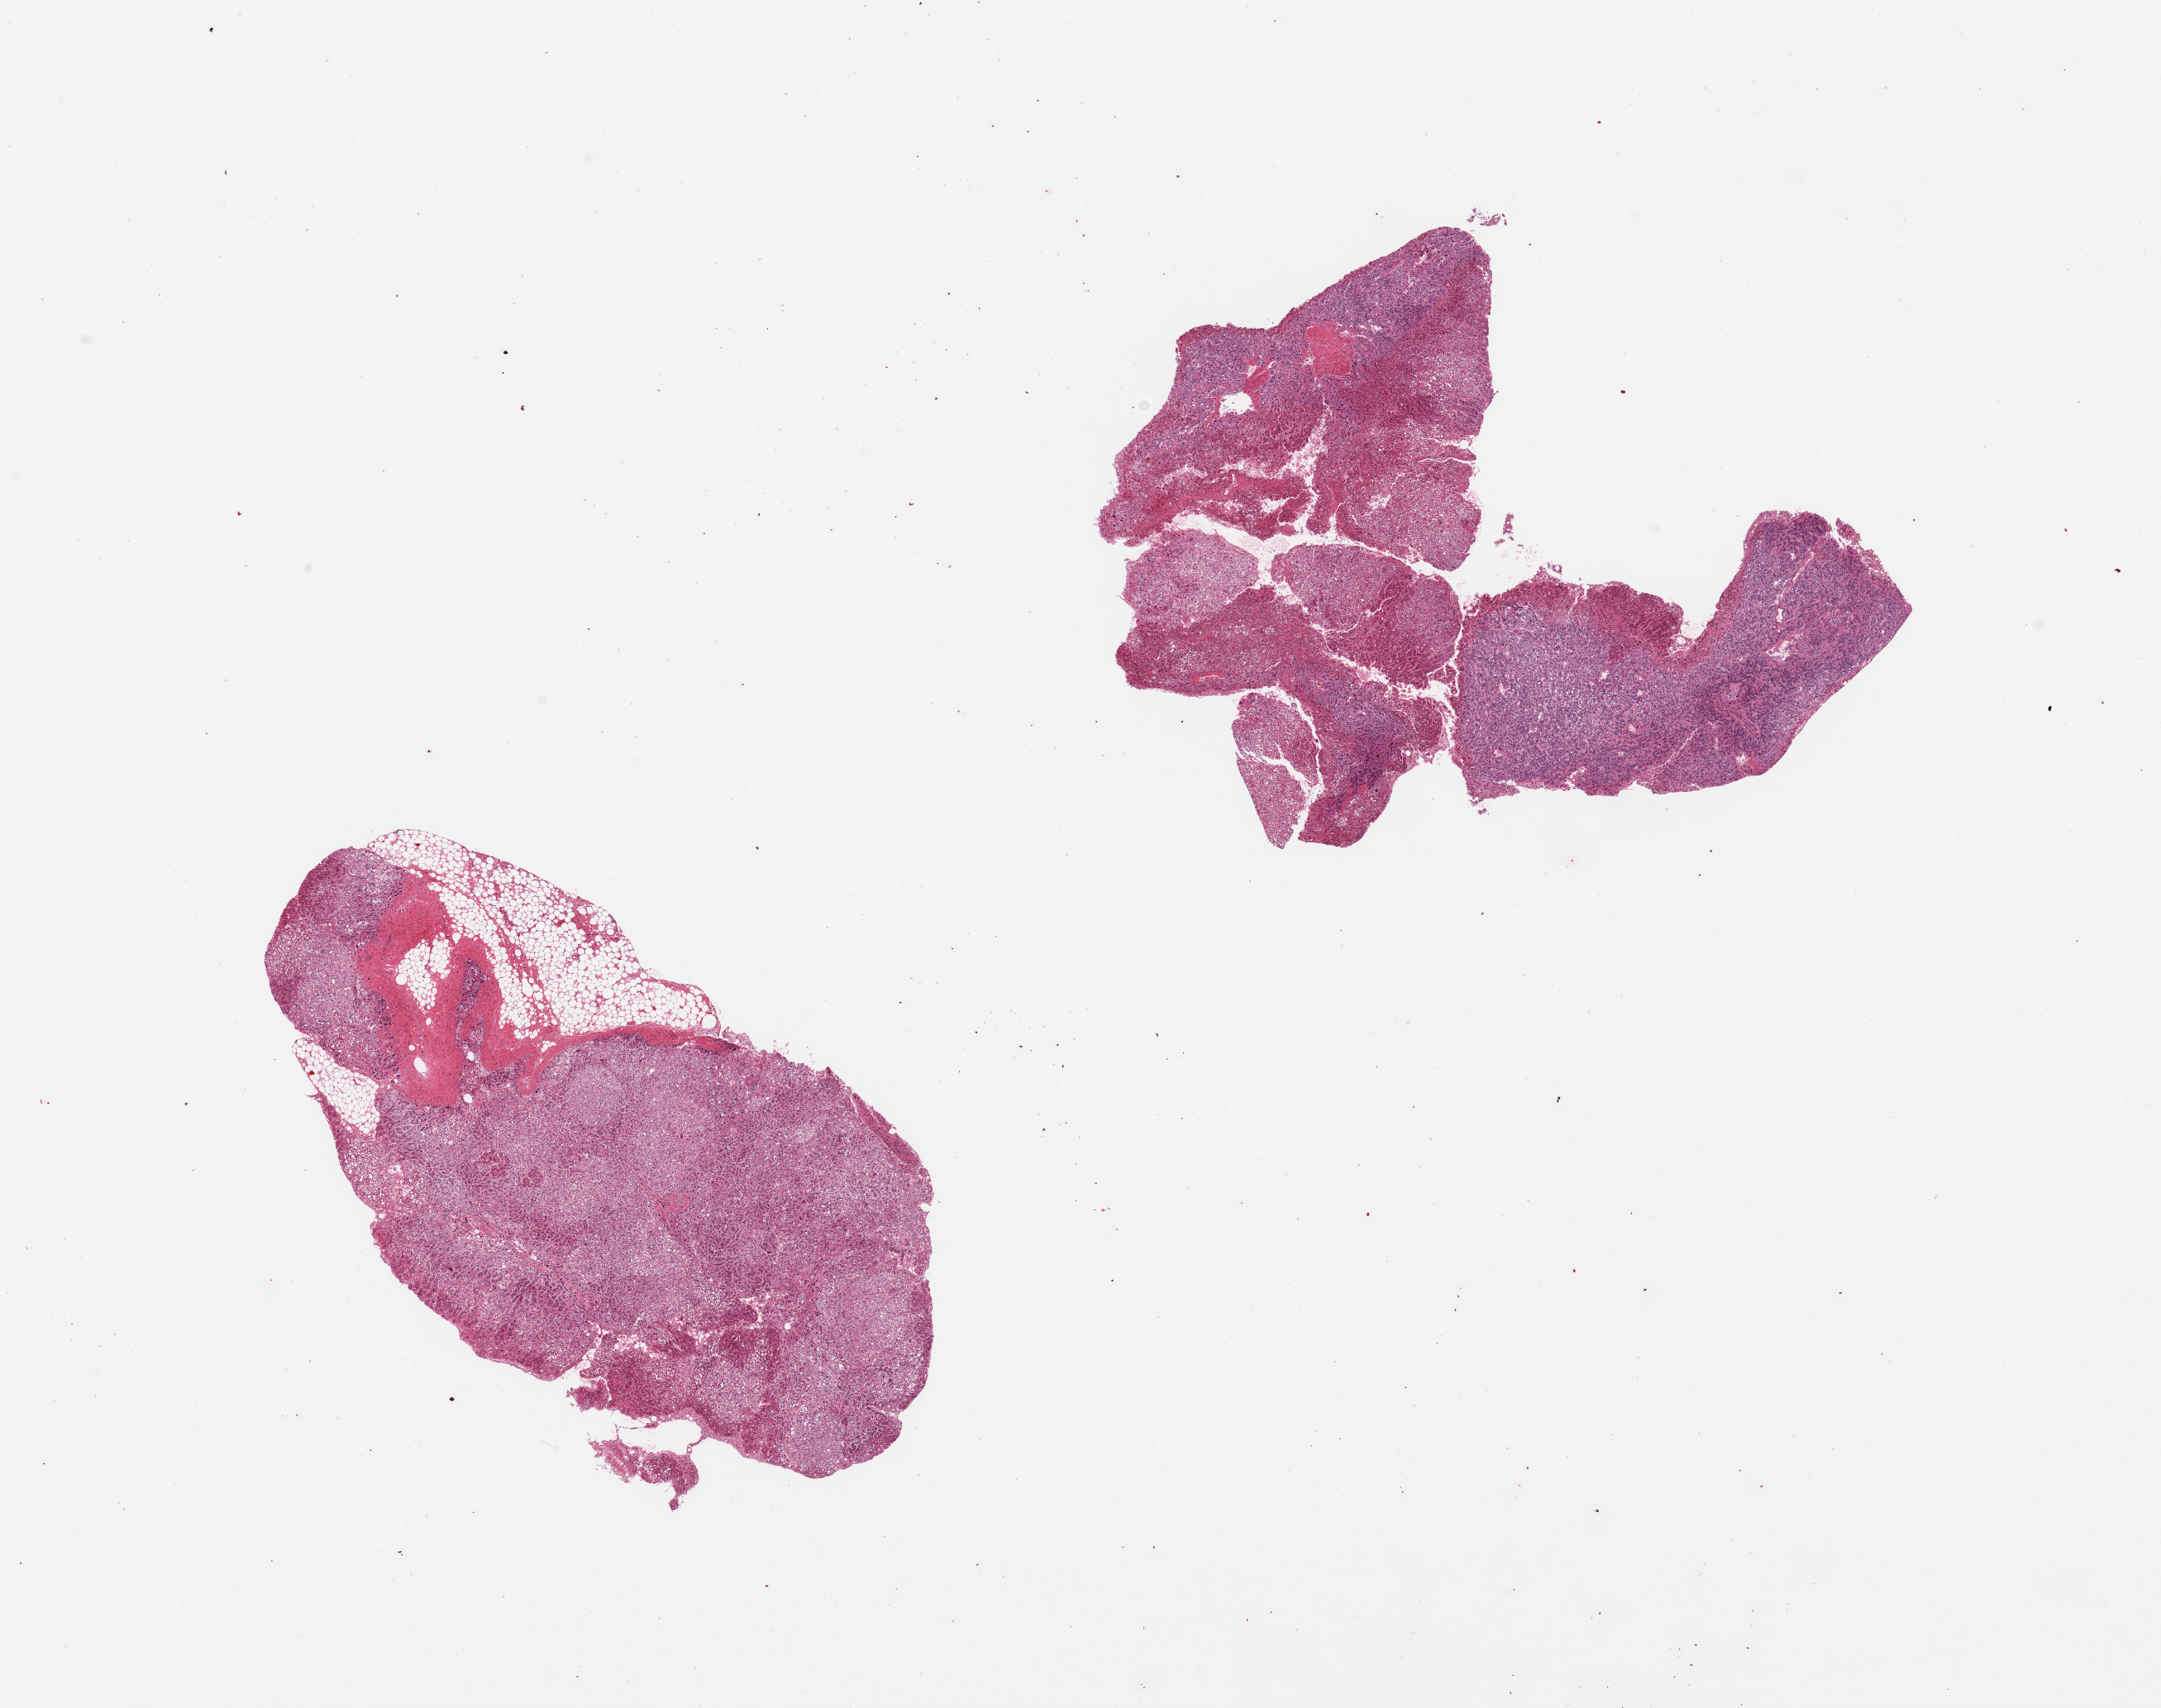
Whole-slide image, hematoxylin and eosin (H&E) stain, low-resolution overview of the scanned area, about 20.7 x 16.3 mm (from a 20x scan); PAXgene-fixed, paraffin-embedded tissue; target tissue: adrenal gland; tissue donor sample. Donor sex: male.
Reviewer comment on this tissue sample: 2 pieces.